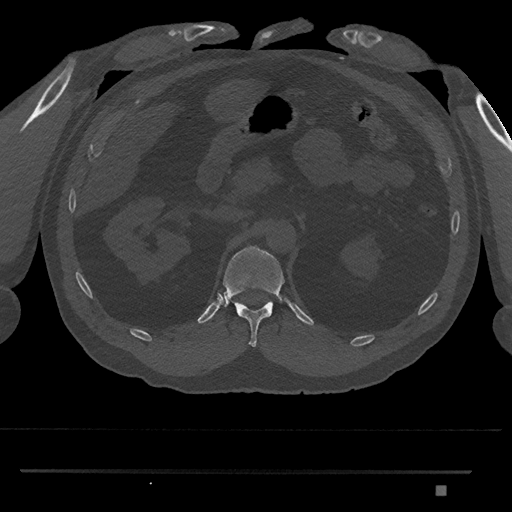
CT including the spine, one axial slice. Position 878 of 1134 along the scan axis. Reconstruction kernel Br40s/3. 120 kVp. Bone window (W 1800 / L 400 HU). 0.5 mm slice thickness. 512 × 512 image matrix, field of view 429 × 429 mm. Male patient, age 65 years. From the clinical record (not read from this slice): primary cancer: prostate.
Structures marked on this image (semi-automatic segmentation, software-assisted and operator-edited):
- T12 vertebra: box from (x=221, y=246) to (x=285, y=347) px